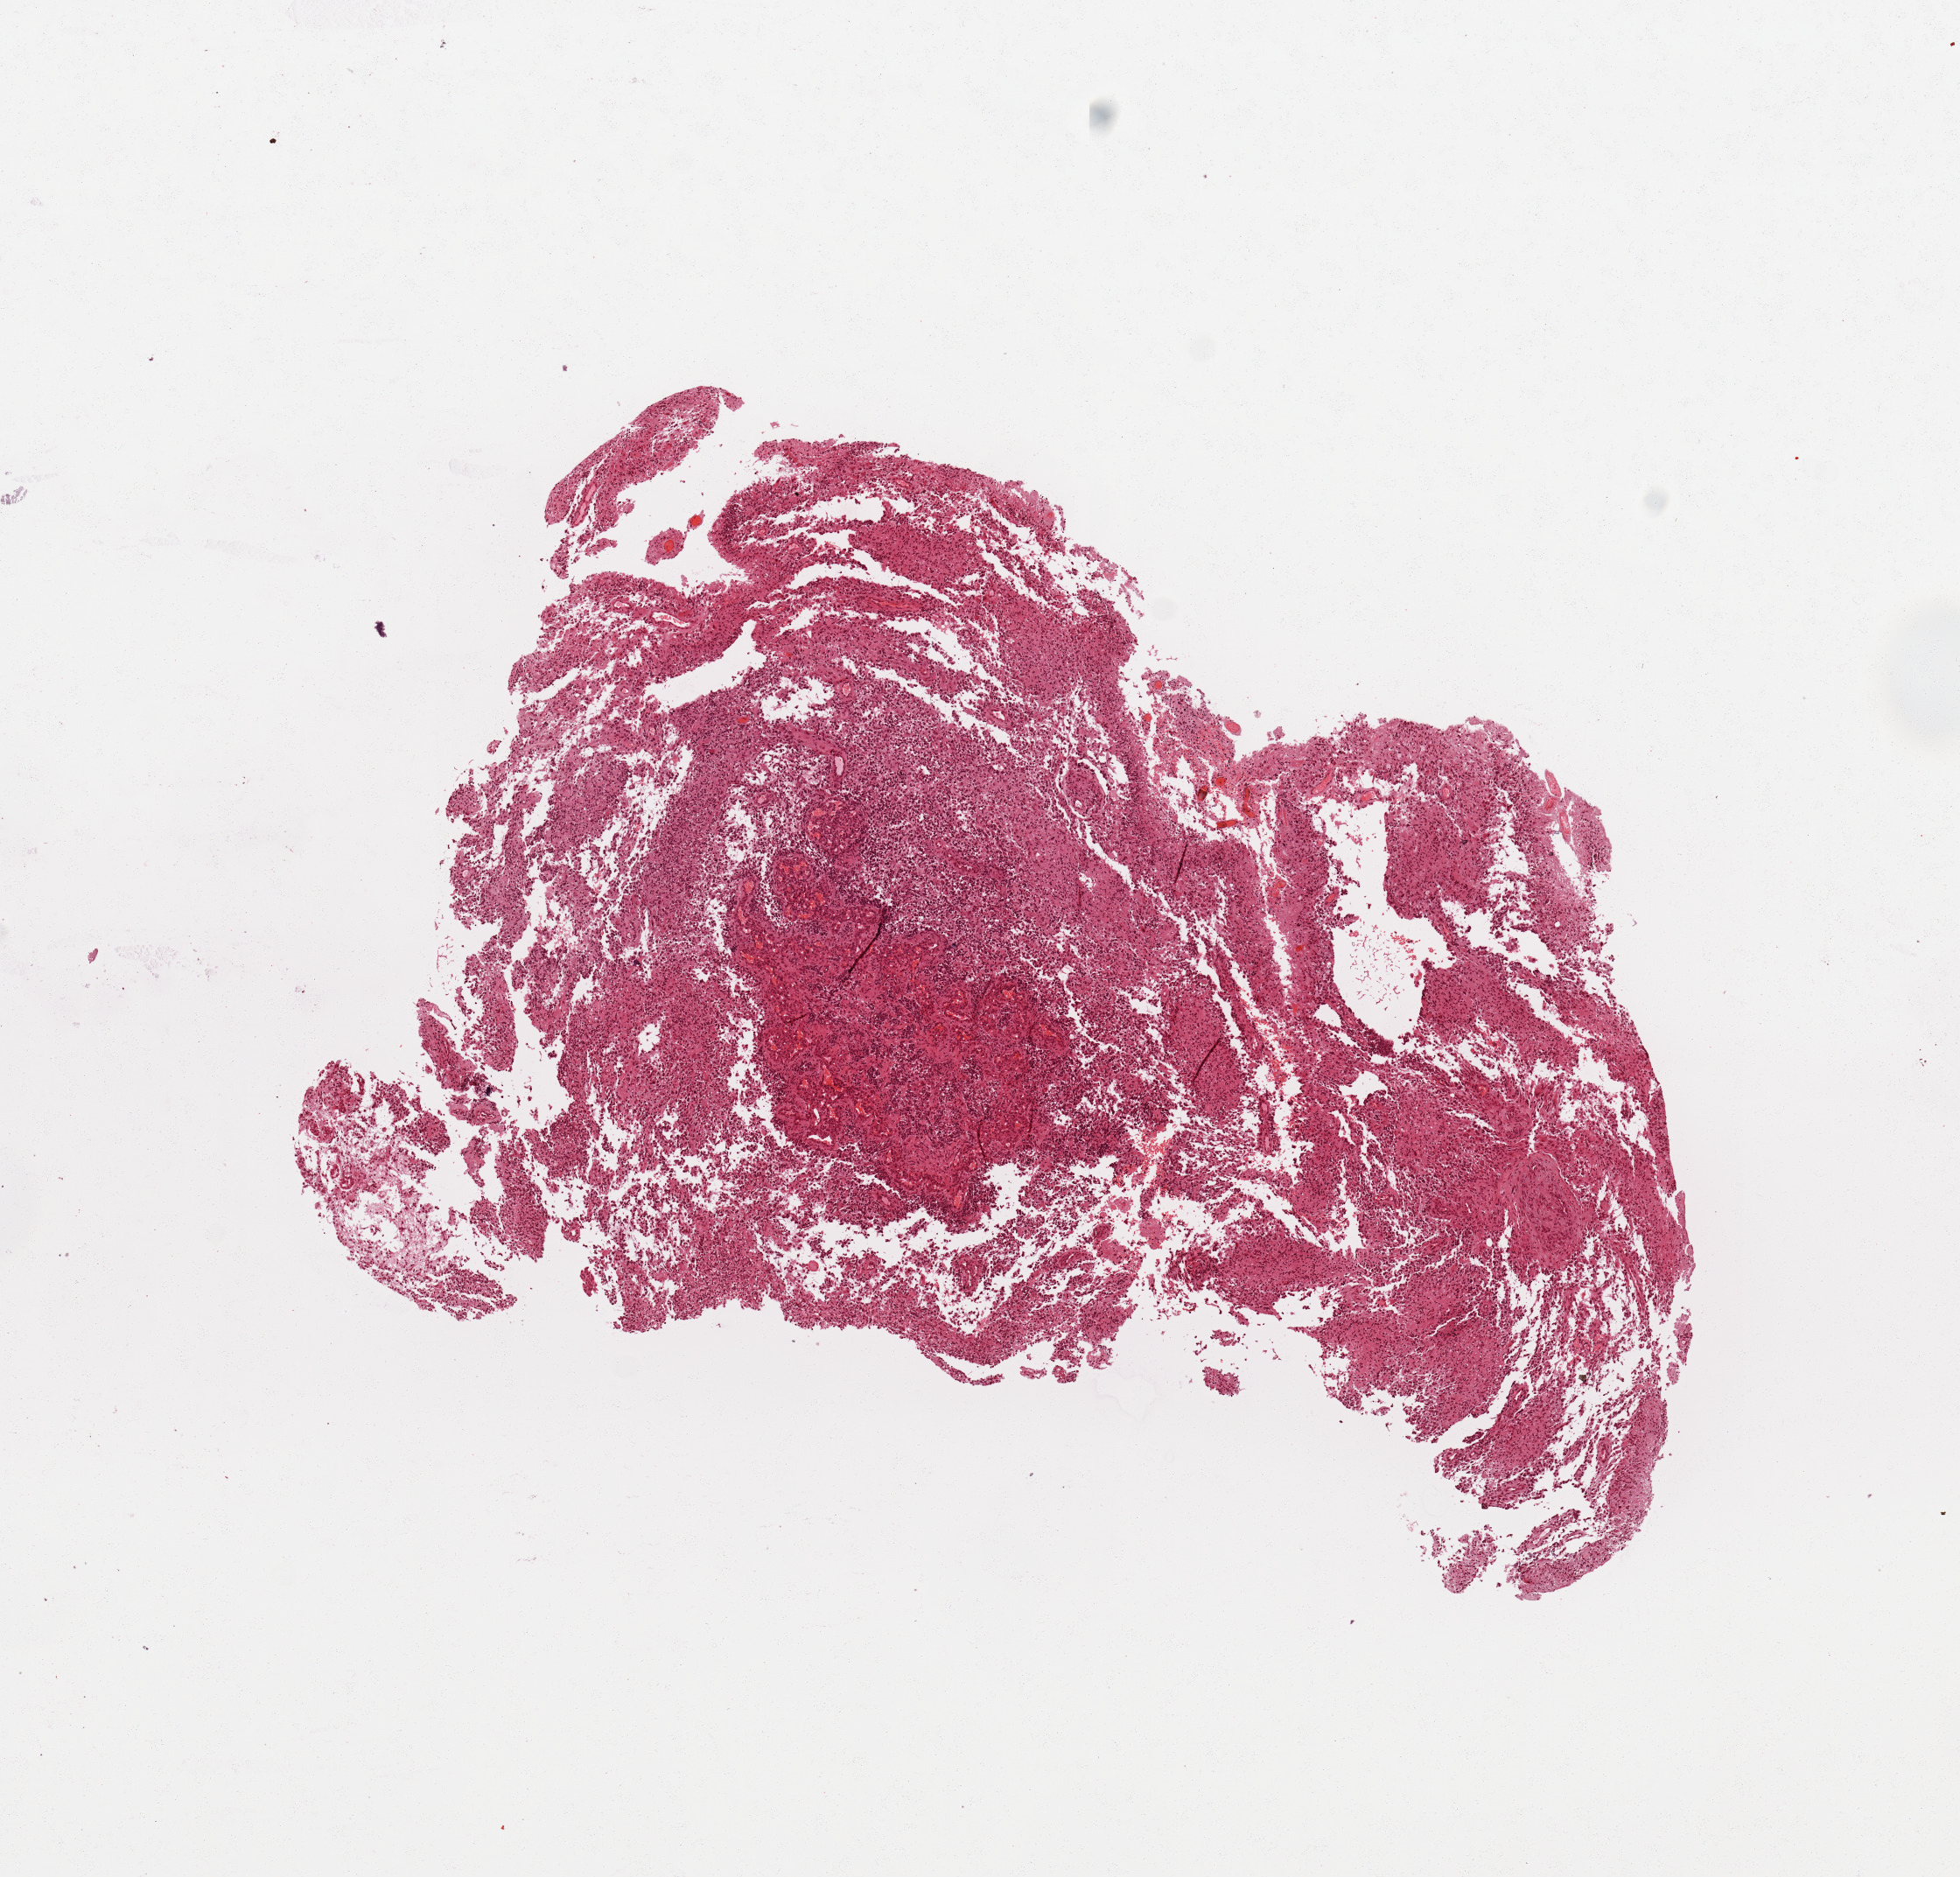
Digitized Hematoxylin and eosin (H&E) stained tissue section (whole slide) — whole scanned area (about 8.9 x 8.5 mm, acquisition: 20x scan) shown as a low-resolution overview. Tumour tissue sample, sampled site: brain. Patient: female, age 48 years. Composition of this section per pathologist review: tumour nuclei 90%, necrosis 3%.
Histologic diagnosis: Glioblastoma.